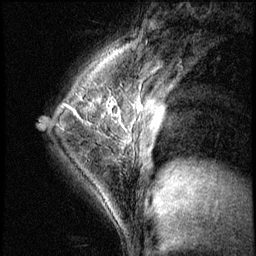
Breast MRI (dynamic contrast-enhanced), one sagittal slice. Slice 40 of 56 in the series (ordered by position). 3 images stored at this slice position (order not interpretable as contrast timing). 1.5 T. TE 4.2 ms, TR 8.7 ms. 2.5 mm slice thickness. 256 × 256 image matrix, field of view 180 × 180 mm. Female patient, age 35 years. From the clinical record (not read from this slice): setting: breast cancer imaged before/during neoadjuvant chemotherapy; receptor status: HER2-positive.
Outlined on this slice (semi-automatically segmented with operator editing):
- analysis volume of interest (the breast-tissue region the enhancement analysis was run in; not a lesion): bounding box [x1, y1, x2, y2] px = [58, 84, 138, 186]
- tumour enhancement mask (voxels above the 140 % enhancement threshold inside the analysis volume of interest): [62, 104, 81, 120]